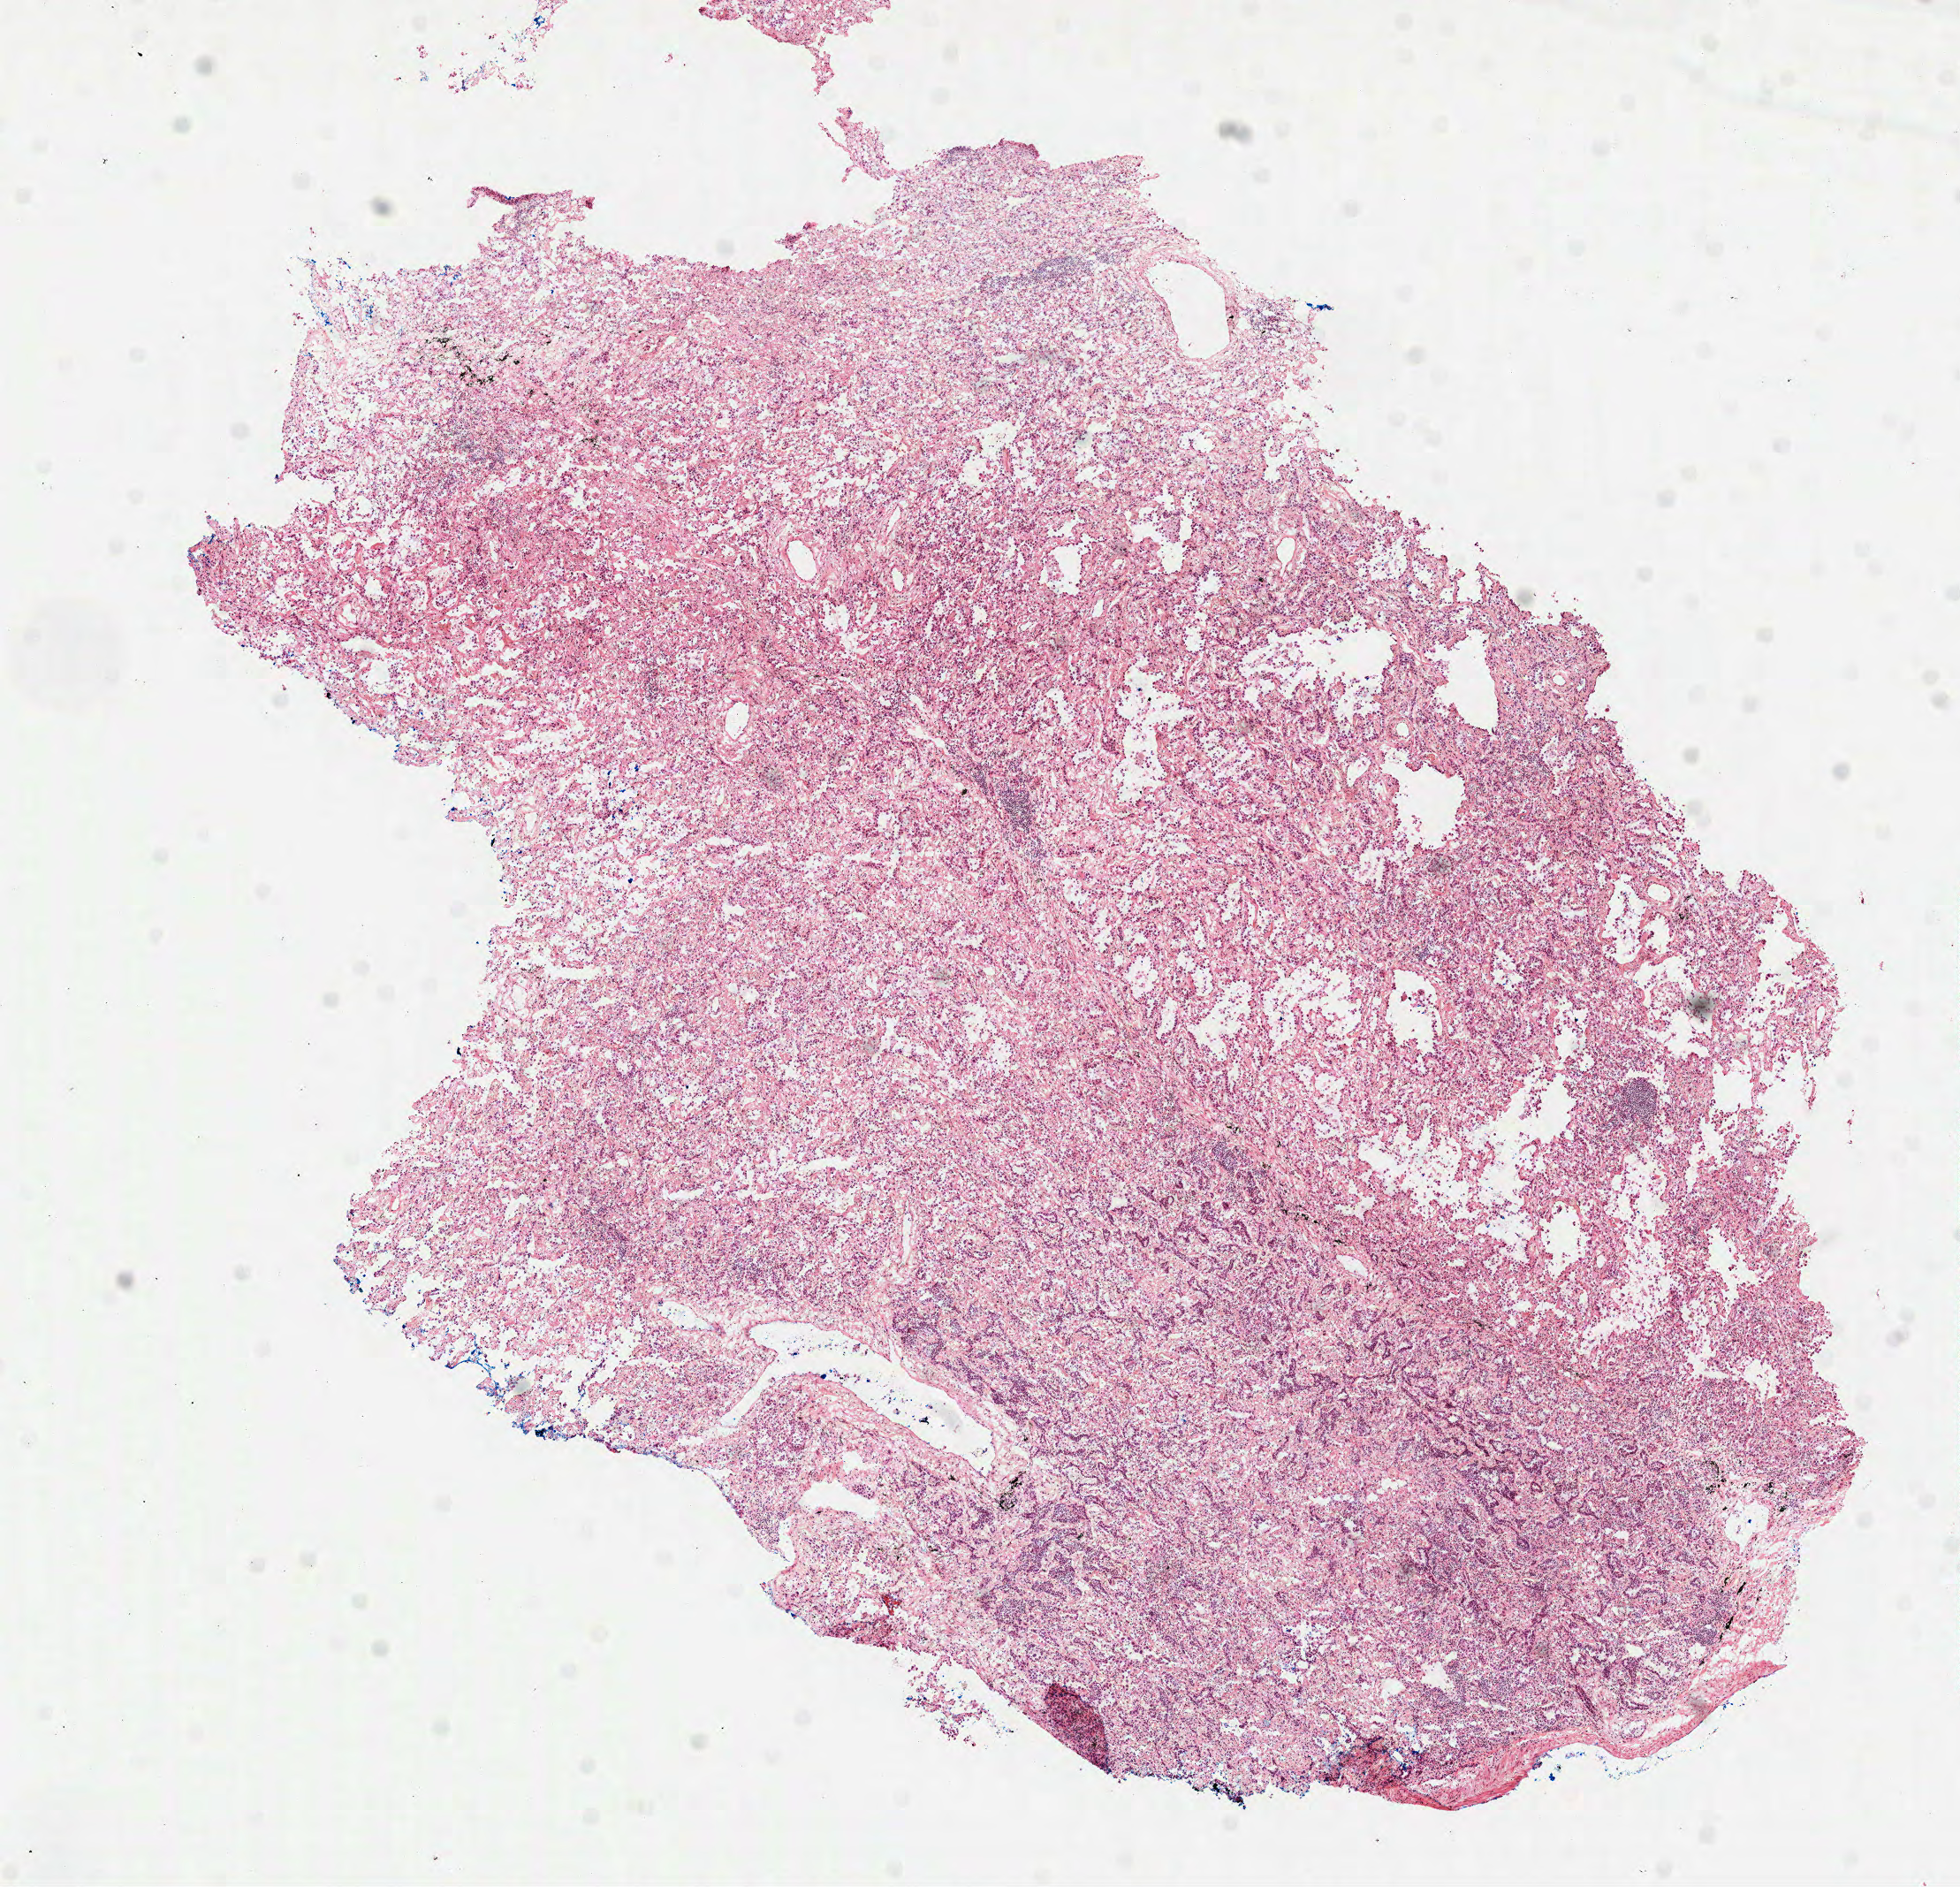
Whole-slide histology image, H&E, a low-resolution overview of the entire scanned area, about 8.9 x 8.6 mm (acquisition: 40x scan). Frozen section from the top of the tissue portion. Primary tumour sample from the lung. Female patient; age at initial diagnosis 76 years. Pathologist review of this section (percent, as recorded): tumour cells 95%, tumour nuclei 65%, normal cells 4%, necrosis 1%. Infiltration values recorded for this section: lymphocyte infiltration 10%, monocyte infiltration 5%.
• TNM: T1 N0 MX
• laterality: left
• AJCC pathologic stage: IA (6th edition)
• diagnosis: Acinar cell carcinoma (upper lobe, lung)